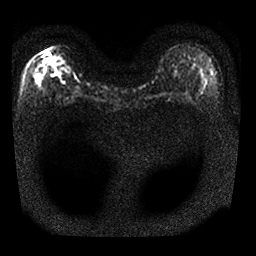
Breast MRI, one axial slice. Position 14 of 25 along the scan axis. Diffusion-weighted series; image 2 of 4 stored at this slice position (different b-values; order by instance number). 1.5 T. 4 mm slice thickness. 256 × 256 image matrix, field of view 300 × 300 mm. Female patient.
Annotated regions visible in this slice (expert manual segmentation):
- tumour on diffusion-weighted imaging: bounding box (x1, y1, x2, y2) in pixels: (46, 51, 53, 58)